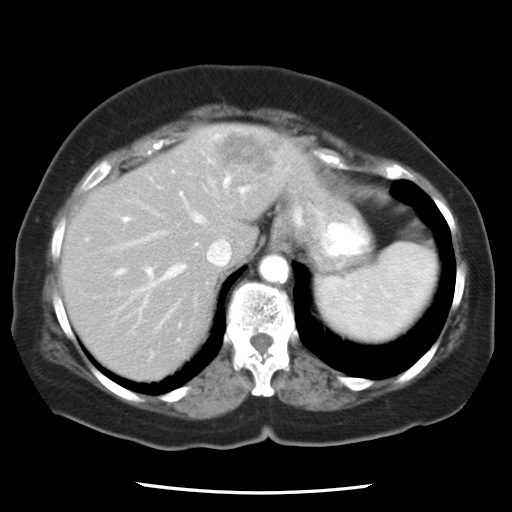
Contrast-enhanced abdominal CT, one axial slice; position 19 of 24 along the scan axis; reconstruction kernel STANDARD; intravenous contrast given; soft-tissue window (W 400 / L 40 HU); 7.5 mm slice thickness; 512 × 512 image matrix, field of view 312 × 312 mm. Female patient, age 71 years. From the clinical record (not read from this slice): diagnosis: colorectal cancer liver metastases, imaged before liver resection; multiple liver metastases: no; largest metastasis: 4.3 cm; chemotherapy before resection: no.
Annotated regions visible in this slice (expert manual segmentation):
- hepatic veins: bounding box (x1, y1, x2, y2) in pixels: (121, 174, 231, 315)
- liver: (61, 125, 305, 380)
- planned liver remnant (the part of the liver to remain after resection): (61, 145, 251, 380)
- portal vein (with intrahepatic branches): (118, 135, 252, 276)
- liver metastasis: (213, 129, 285, 177)